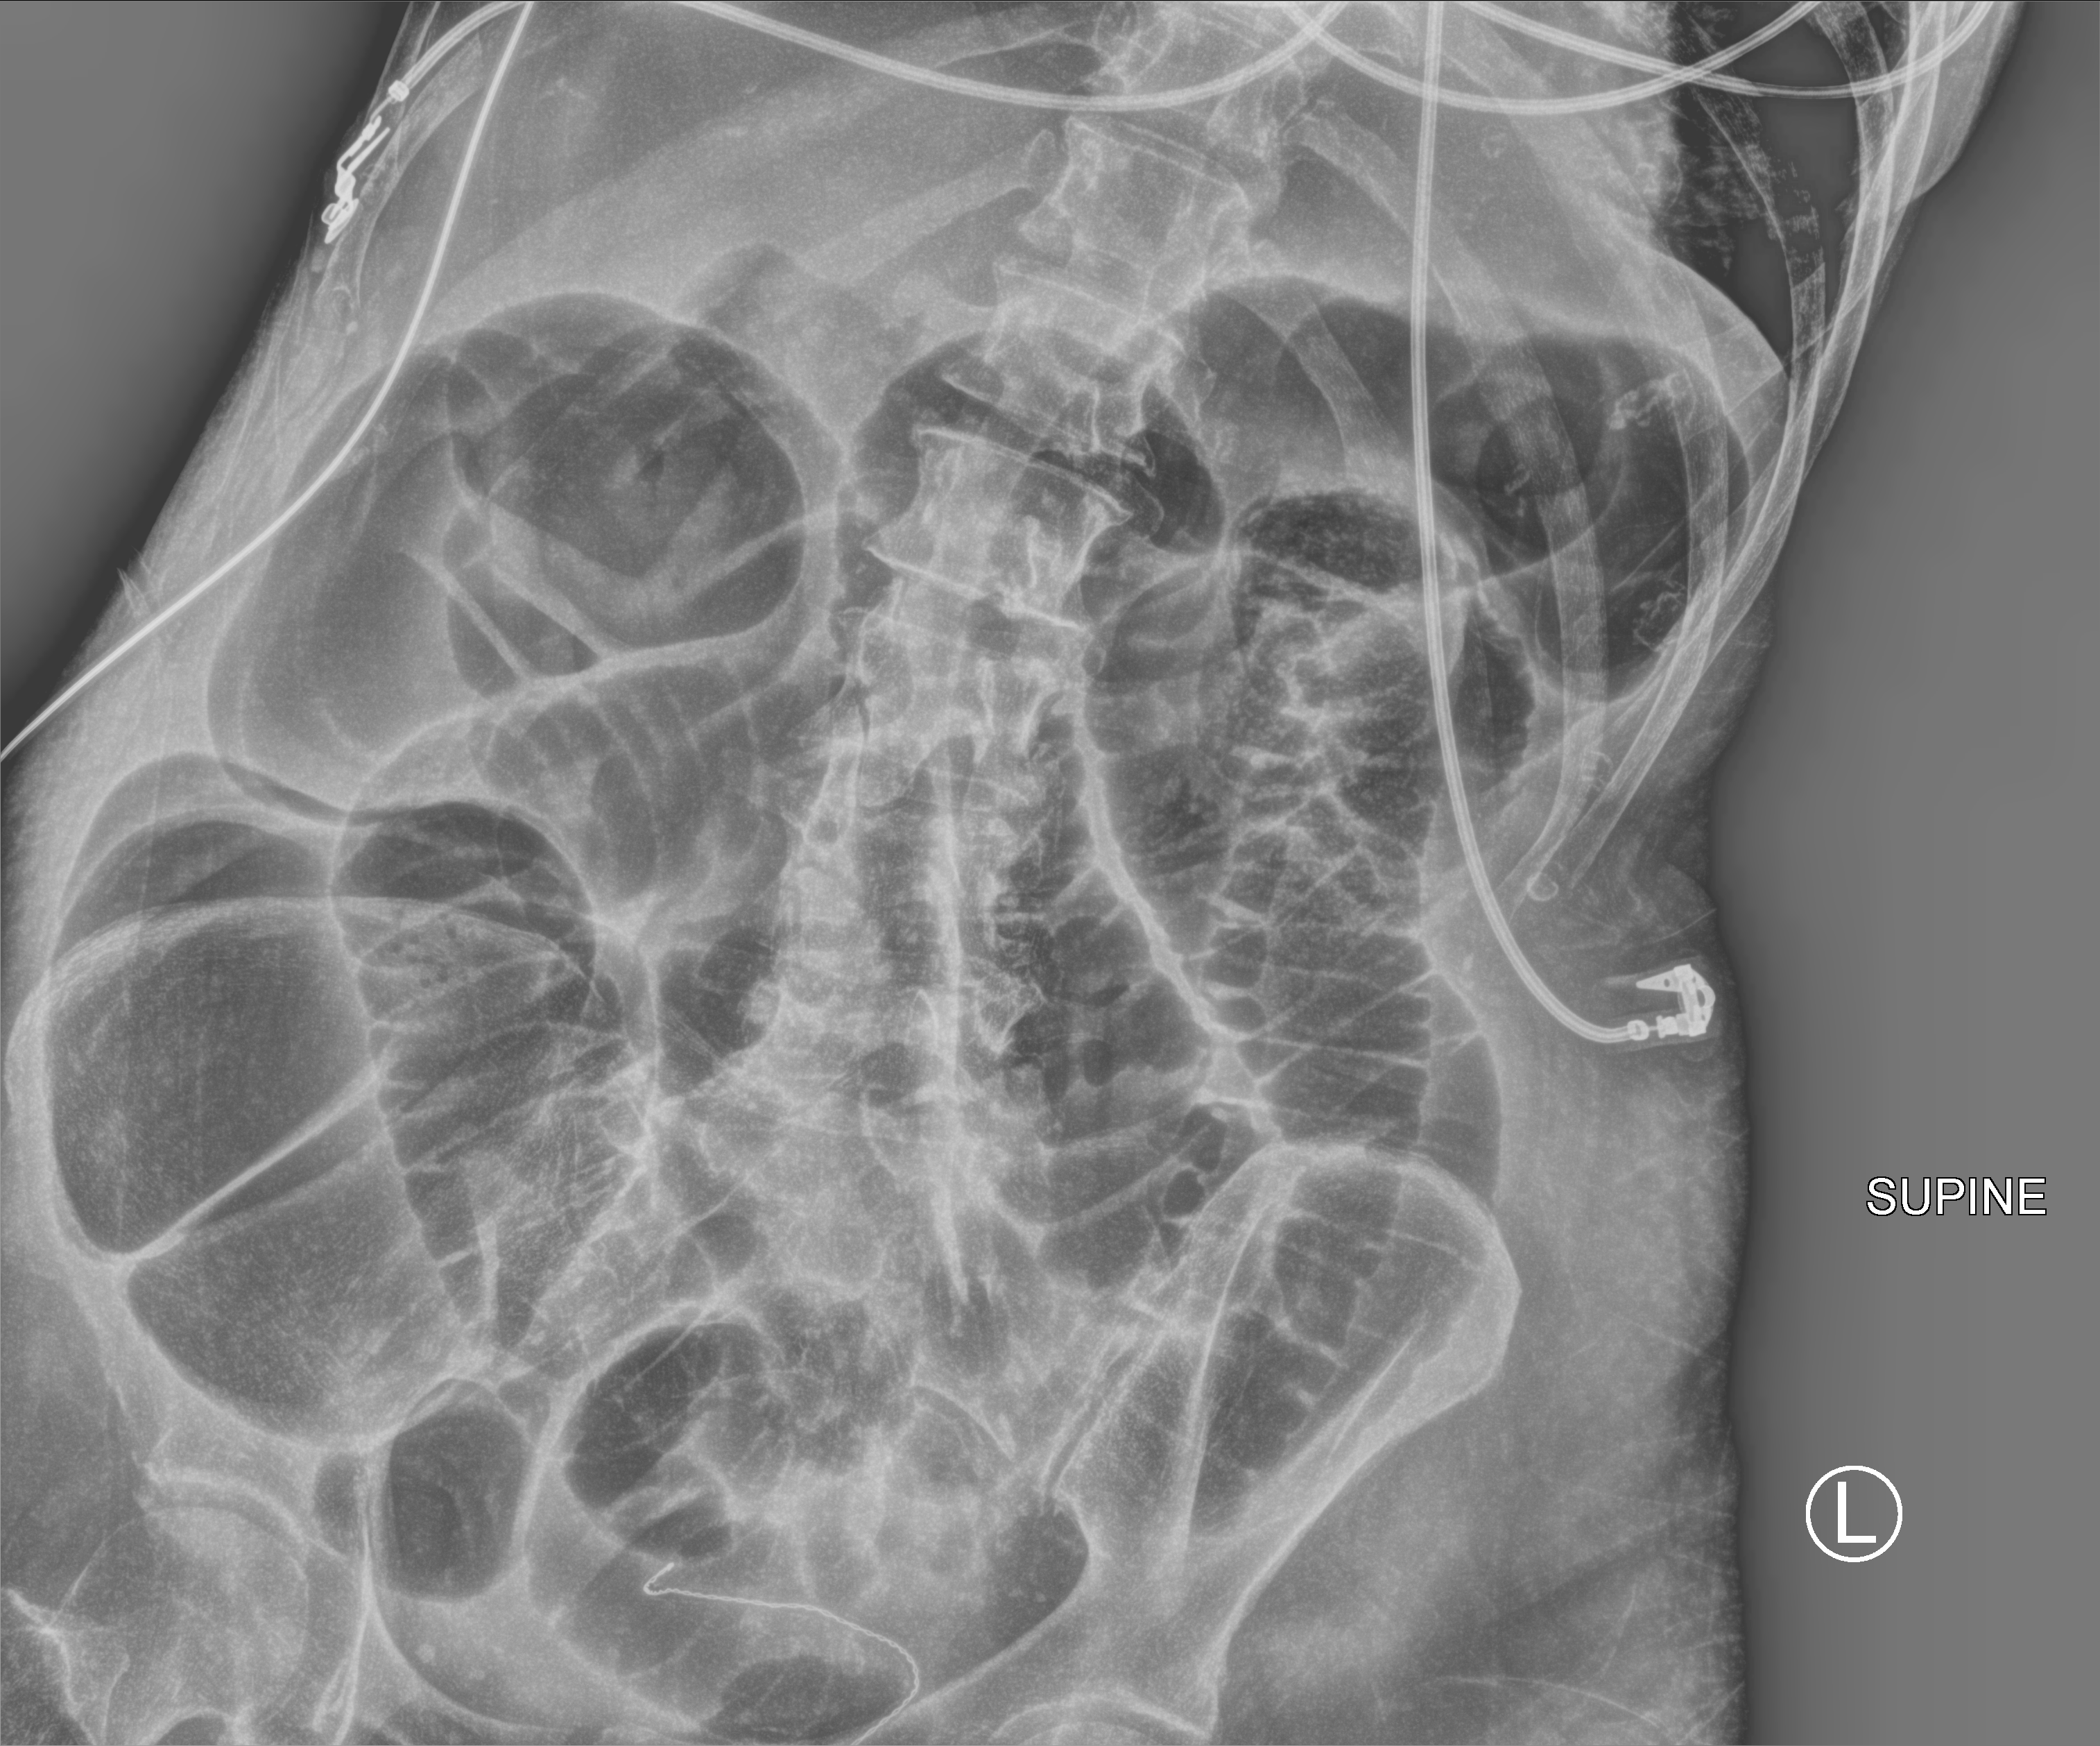
Abdomen X-ray (portable), anteroposterior (AP) projection. Female patient hospitalised with COVID-19, age 60–74 years.
Admission-level facts for this patient (not findings on this image; timing relative to this image not recorded):
- admitted to intensive care during this hospital stay: yes
- length of hospital stay: 38 days
- mechanically ventilated during this hospital stay: yes